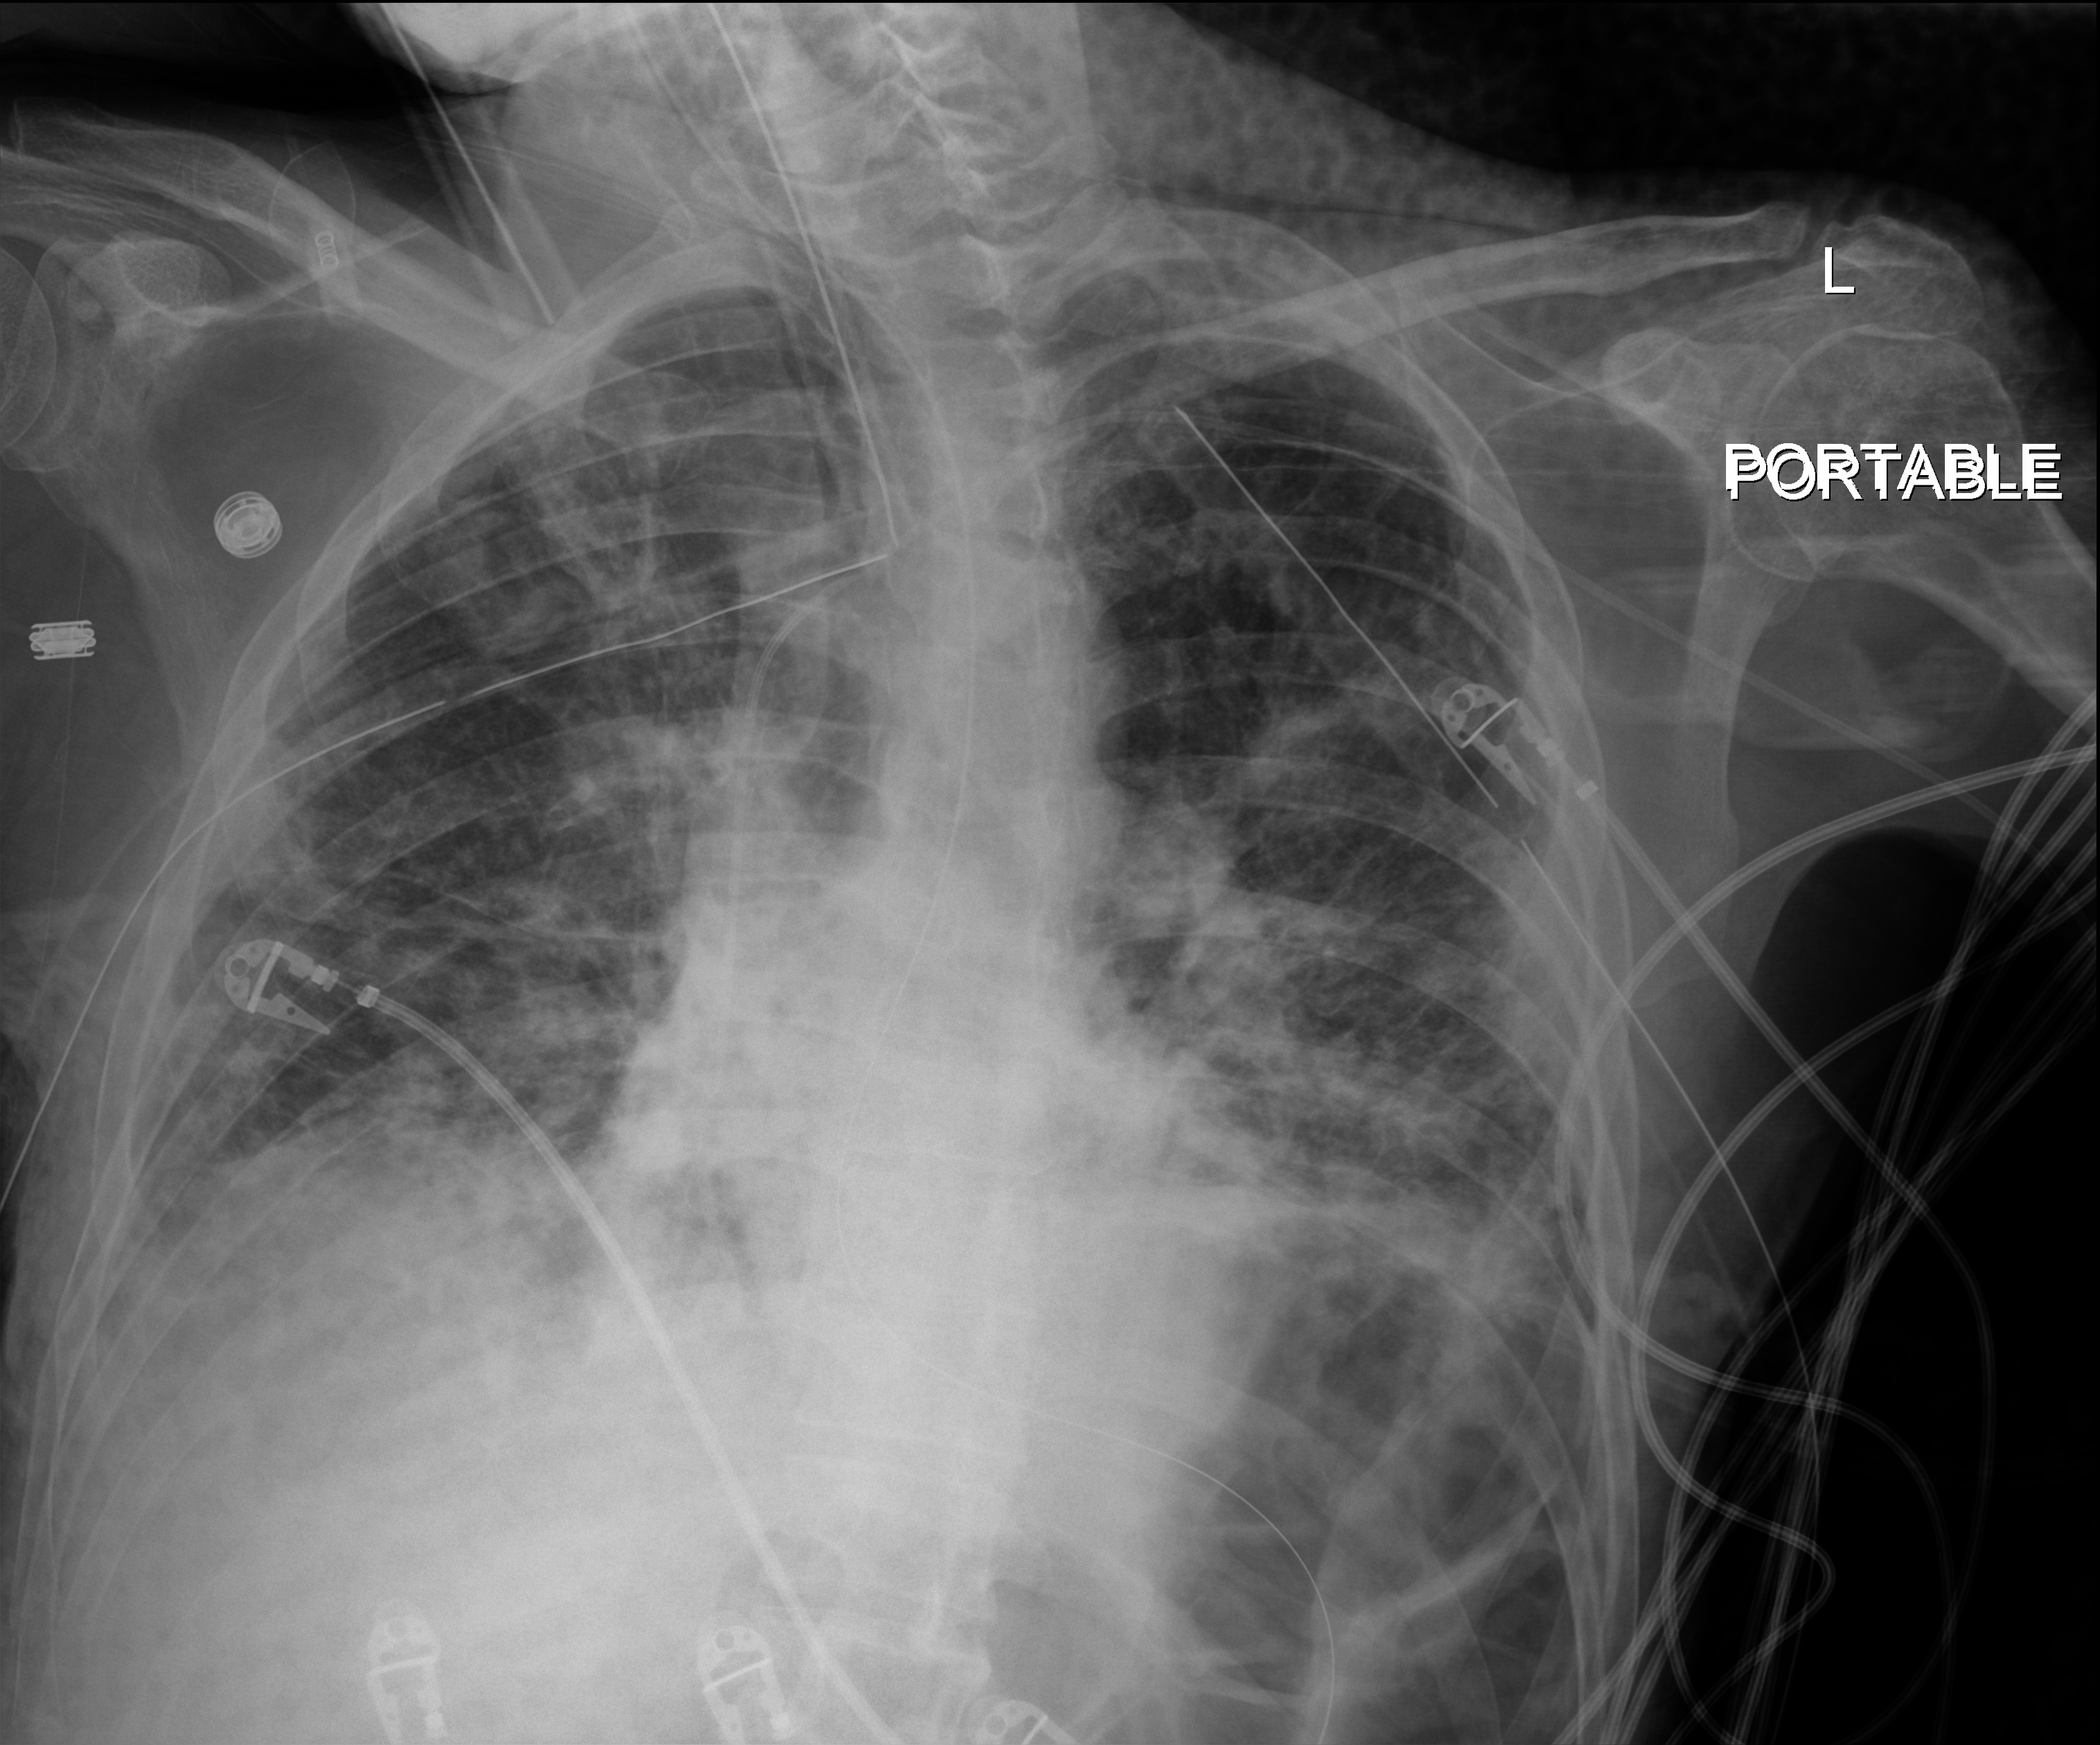
Chest X-ray (portable); anteroposterior (AP) projection. Patient hospitalised with COVID-19; male, aged 18–59 years.
Admission-level facts for this patient (not findings on this image; timing relative to this image not recorded): diabetes (admission record): yes.